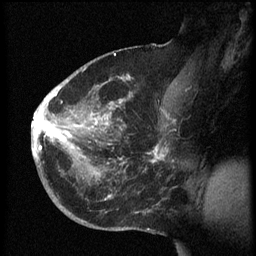
Breast MRI (dynamic contrast-enhanced), one sagittal slice; position 36 of 60 along the scan axis; dynamic contrast-enhanced series, image 2 of 3 at this slice position (ordered by acquisition); 1.5 T; TE 4.2 ms, TR 8.4 ms; 256 × 256 image matrix, field of view 200 × 200 mm. Patient: female, 38 years. Case-level facts recorded for this patient, not image findings: setting: breast cancer imaged before/during neoadjuvant chemotherapy; receptor status: HER2-positive.
Outlined on this slice (semi-automatically segmented with operator editing):
- analysis volume of interest (the breast-tissue region the enhancement analysis was run in; not a lesion): bounding box (x1, y1, x2, y2) in pixels: (32, 74, 173, 202)
- tumour enhancement mask (voxels above the 70 % enhancement threshold inside the analysis volume of interest): (32, 76, 168, 201)